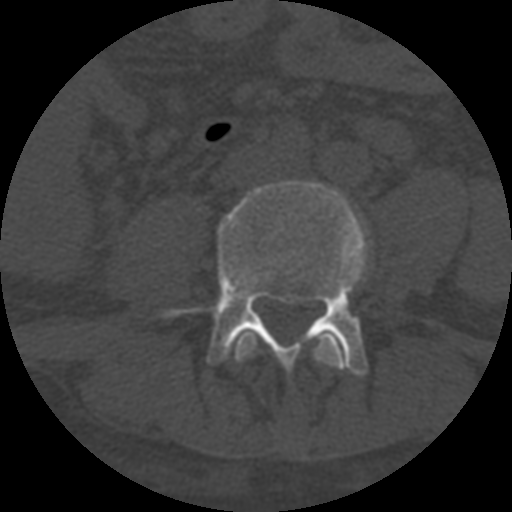
CT including the spine, one axial slice. Position 215 of 708 along the scan axis. Reconstruction kernel STANDARD. One of 3 acquisitions stored at this slice position. Bone window (W 1800 / L 400 HU). 1.25 mm slice thickness. 512 × 512 image matrix, field of view 160 × 160 mm. Patient age 55 years. Case-level facts recorded for this patient, not image findings: primary cancer: colon; vertebrae with lytic lesions (as recorded): T12, L1, L5.
Structures marked on this image (semi-automatically segmented with operator editing):
- L3 vertebra: bounding box [x1, y1, x2, y2] px = [234, 330, 347, 370]
- L4 vertebra: [160, 180, 371, 376]